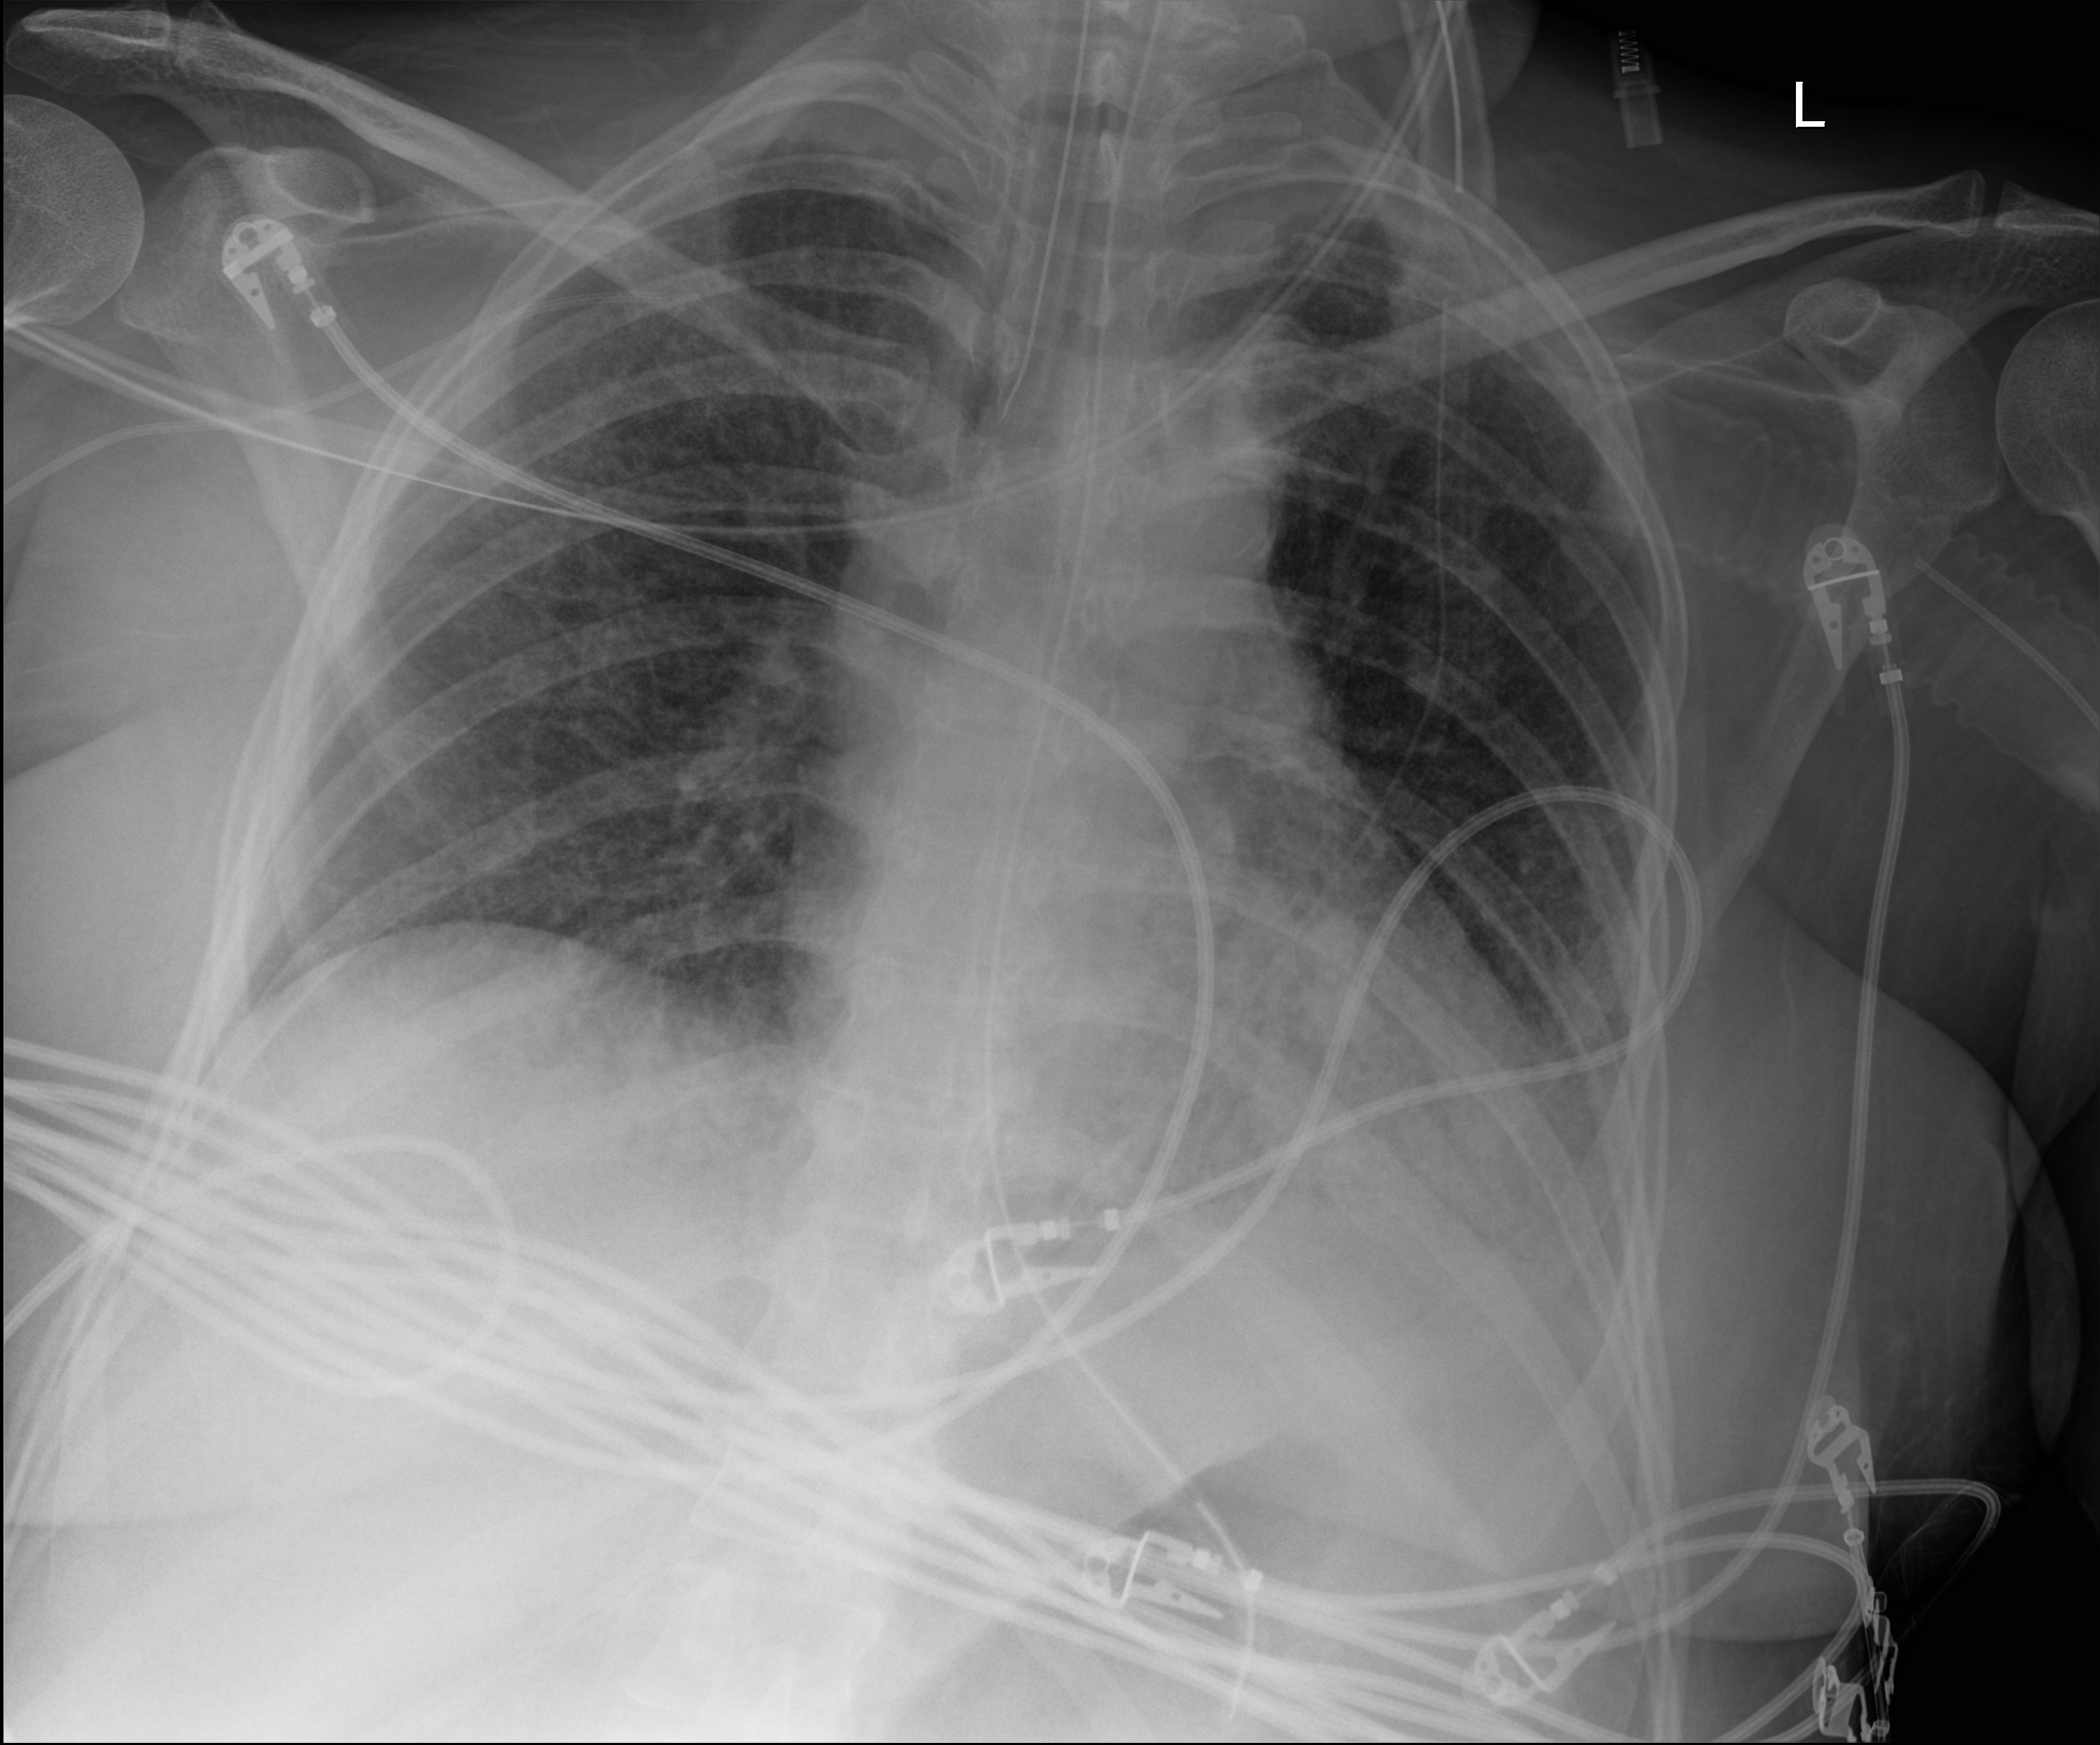
Chest radiograph (digital radiography); anteroposterior (AP) projection. Patient hospitalised with COVID-19; female, aged 18–59 years.
Admission-level facts for this patient (not findings on this image; timing relative to this image not recorded):
- mechanically ventilated during this hospital stay: yes
- admitted to intensive care during this hospital stay: yes